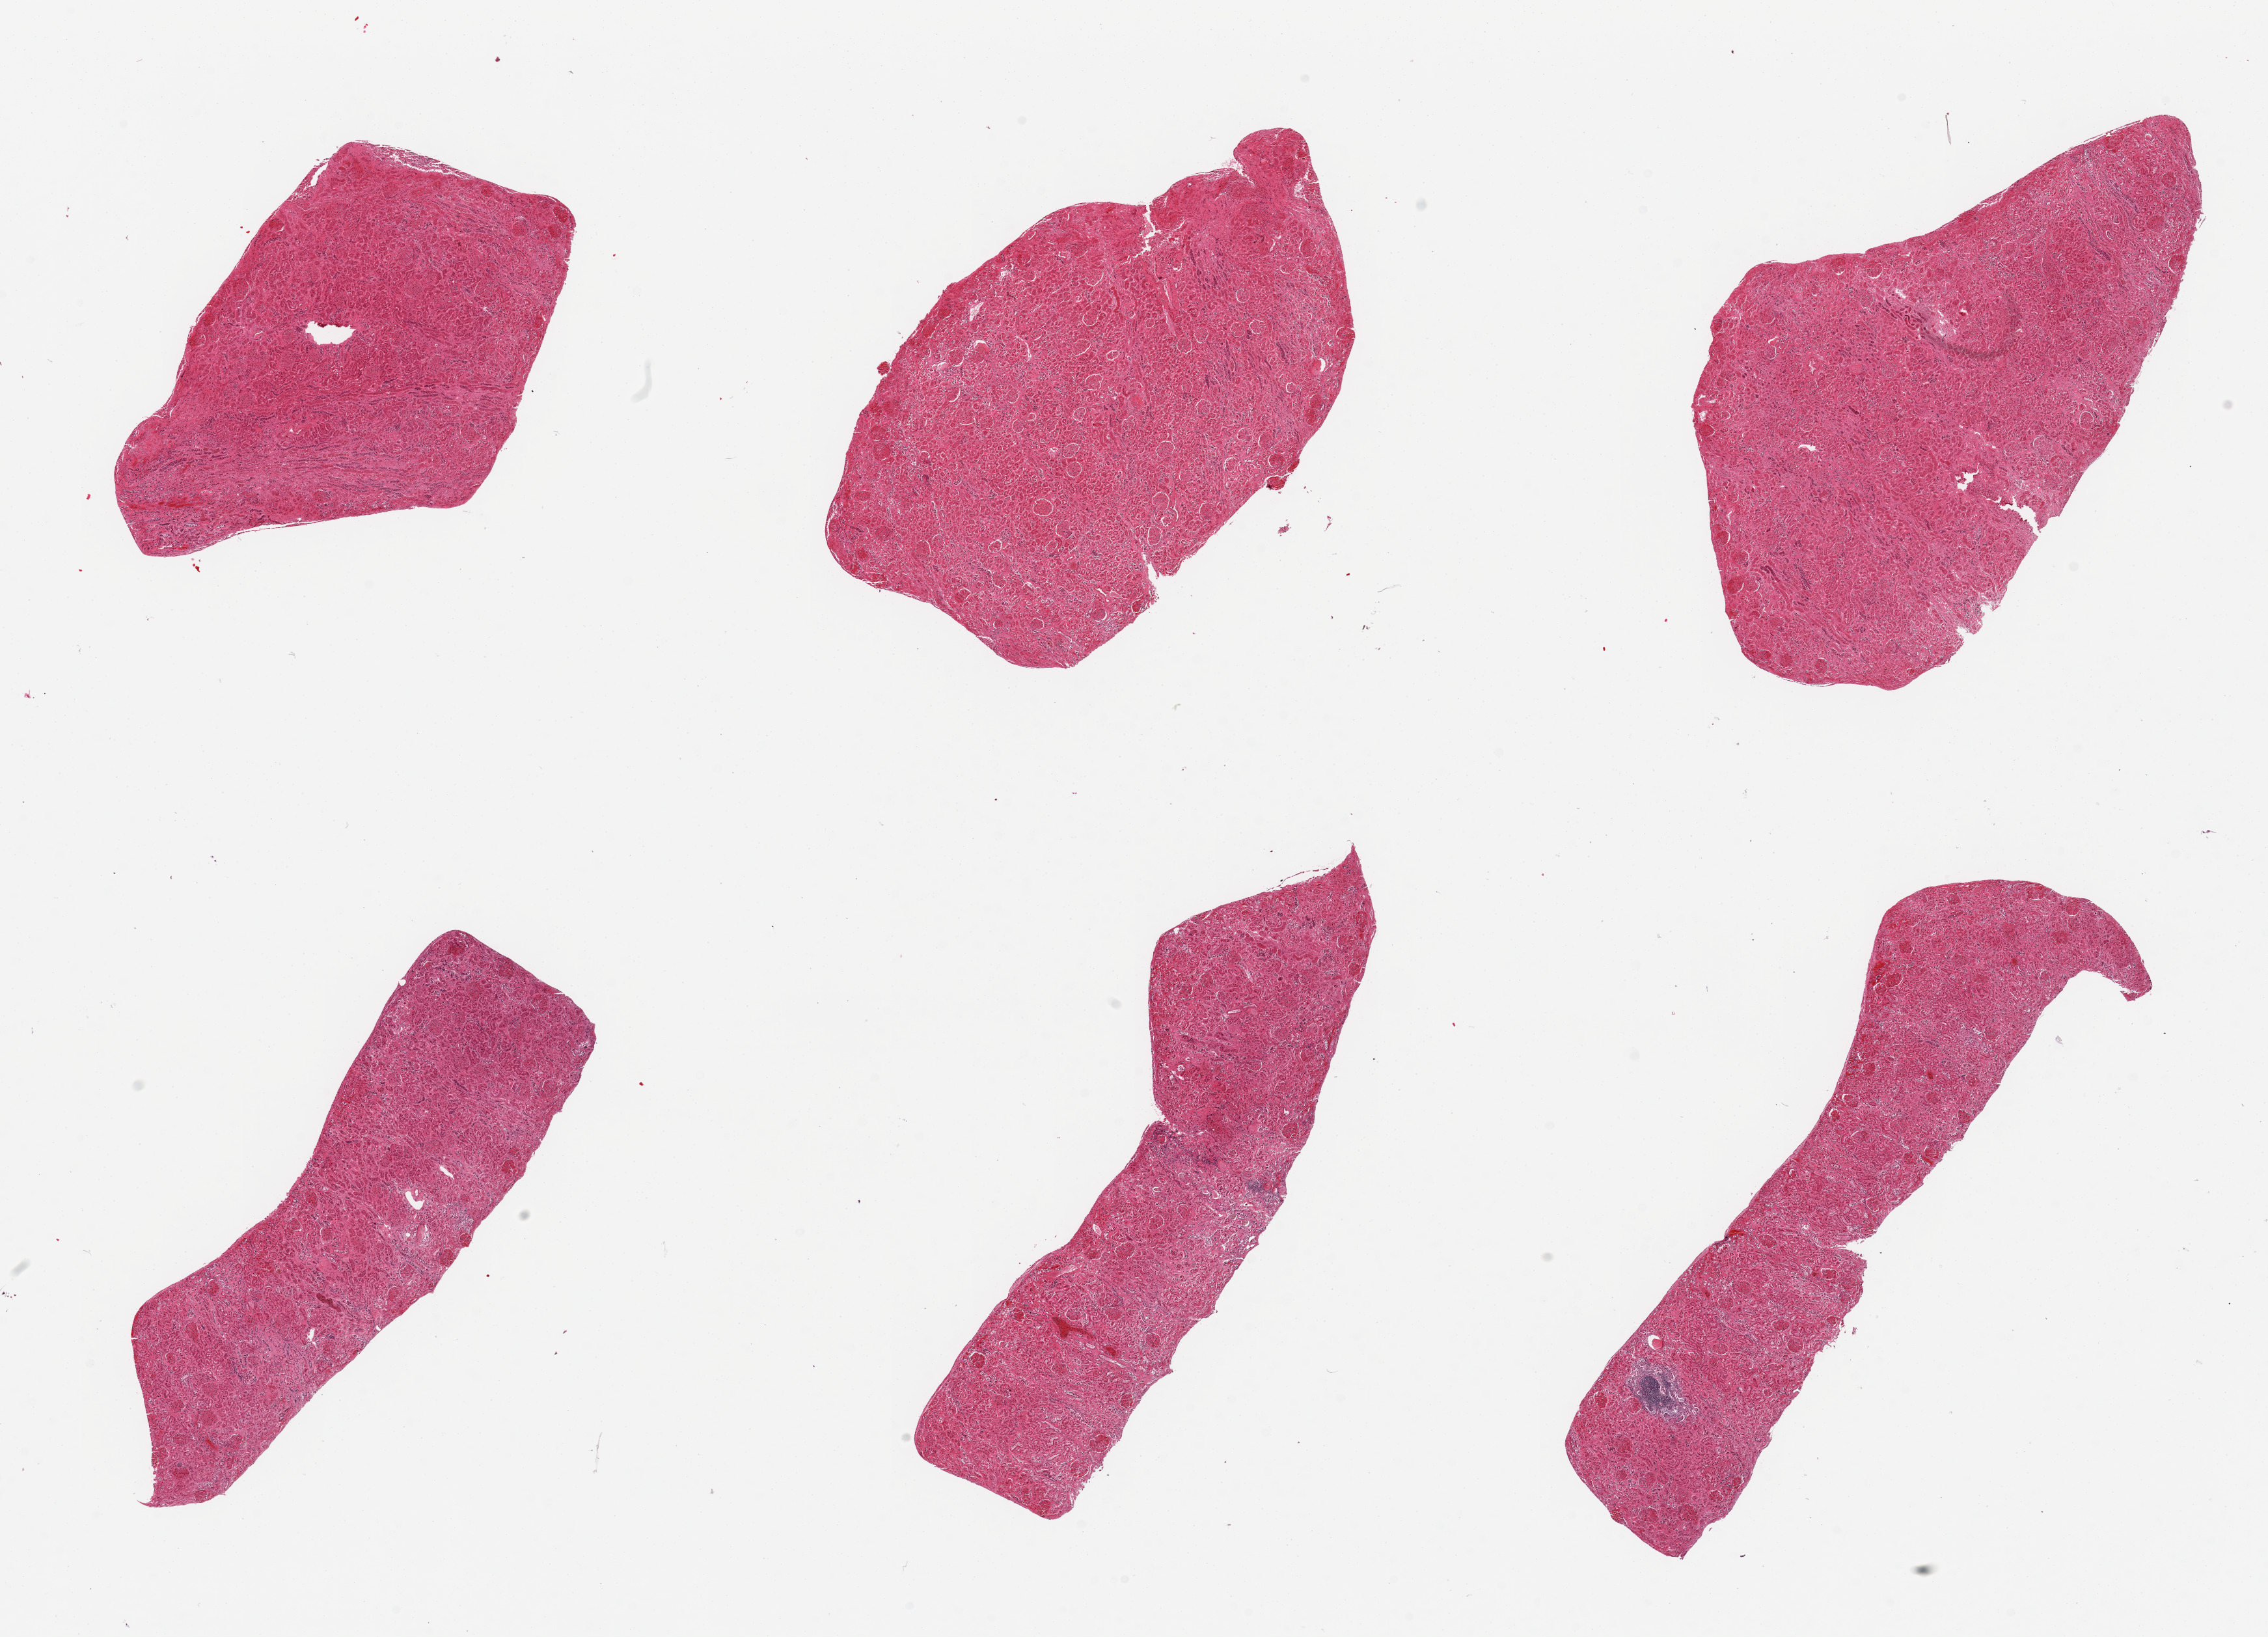
Haematoxylin and eosin whole-slide image, brightfield — a low-resolution overview of the entire scanned area, about 27.6 x 19.9 mm, PAXgene-fixed, paraffin-embedded tissue, section of renal cortex (target tissue), tissue donor sample. Male donor.
Review note (as recorded): 6 pieces, severe autolysis, focus of chronic inflammation.